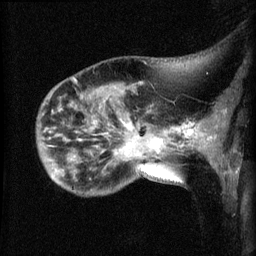
Breast MRI (dynamic contrast-enhanced), one sagittal slice; slice 16 of 60 in the series (ordered by position); dynamic contrast-enhanced series, image 2 of 3 at this slice position (ordered by acquisition); 1.5 T; TE 4.2 ms, TR 8.2 ms; 2.1 mm slice thickness; 256 × 256 image matrix, field of view 180 × 180 mm. Female patient, age 50 years.
Structures marked on this image (semi-automatic segmentation, software-assisted and operator-edited):
- analysis volume of interest (the breast-tissue region the enhancement analysis was run in; not a lesion): bounding box <38,81,169,195> (left, top, right, bottom; pixels)
- tumour enhancement mask (voxels above the 70 % enhancement threshold inside the analysis volume of interest): <130,126,168,153>